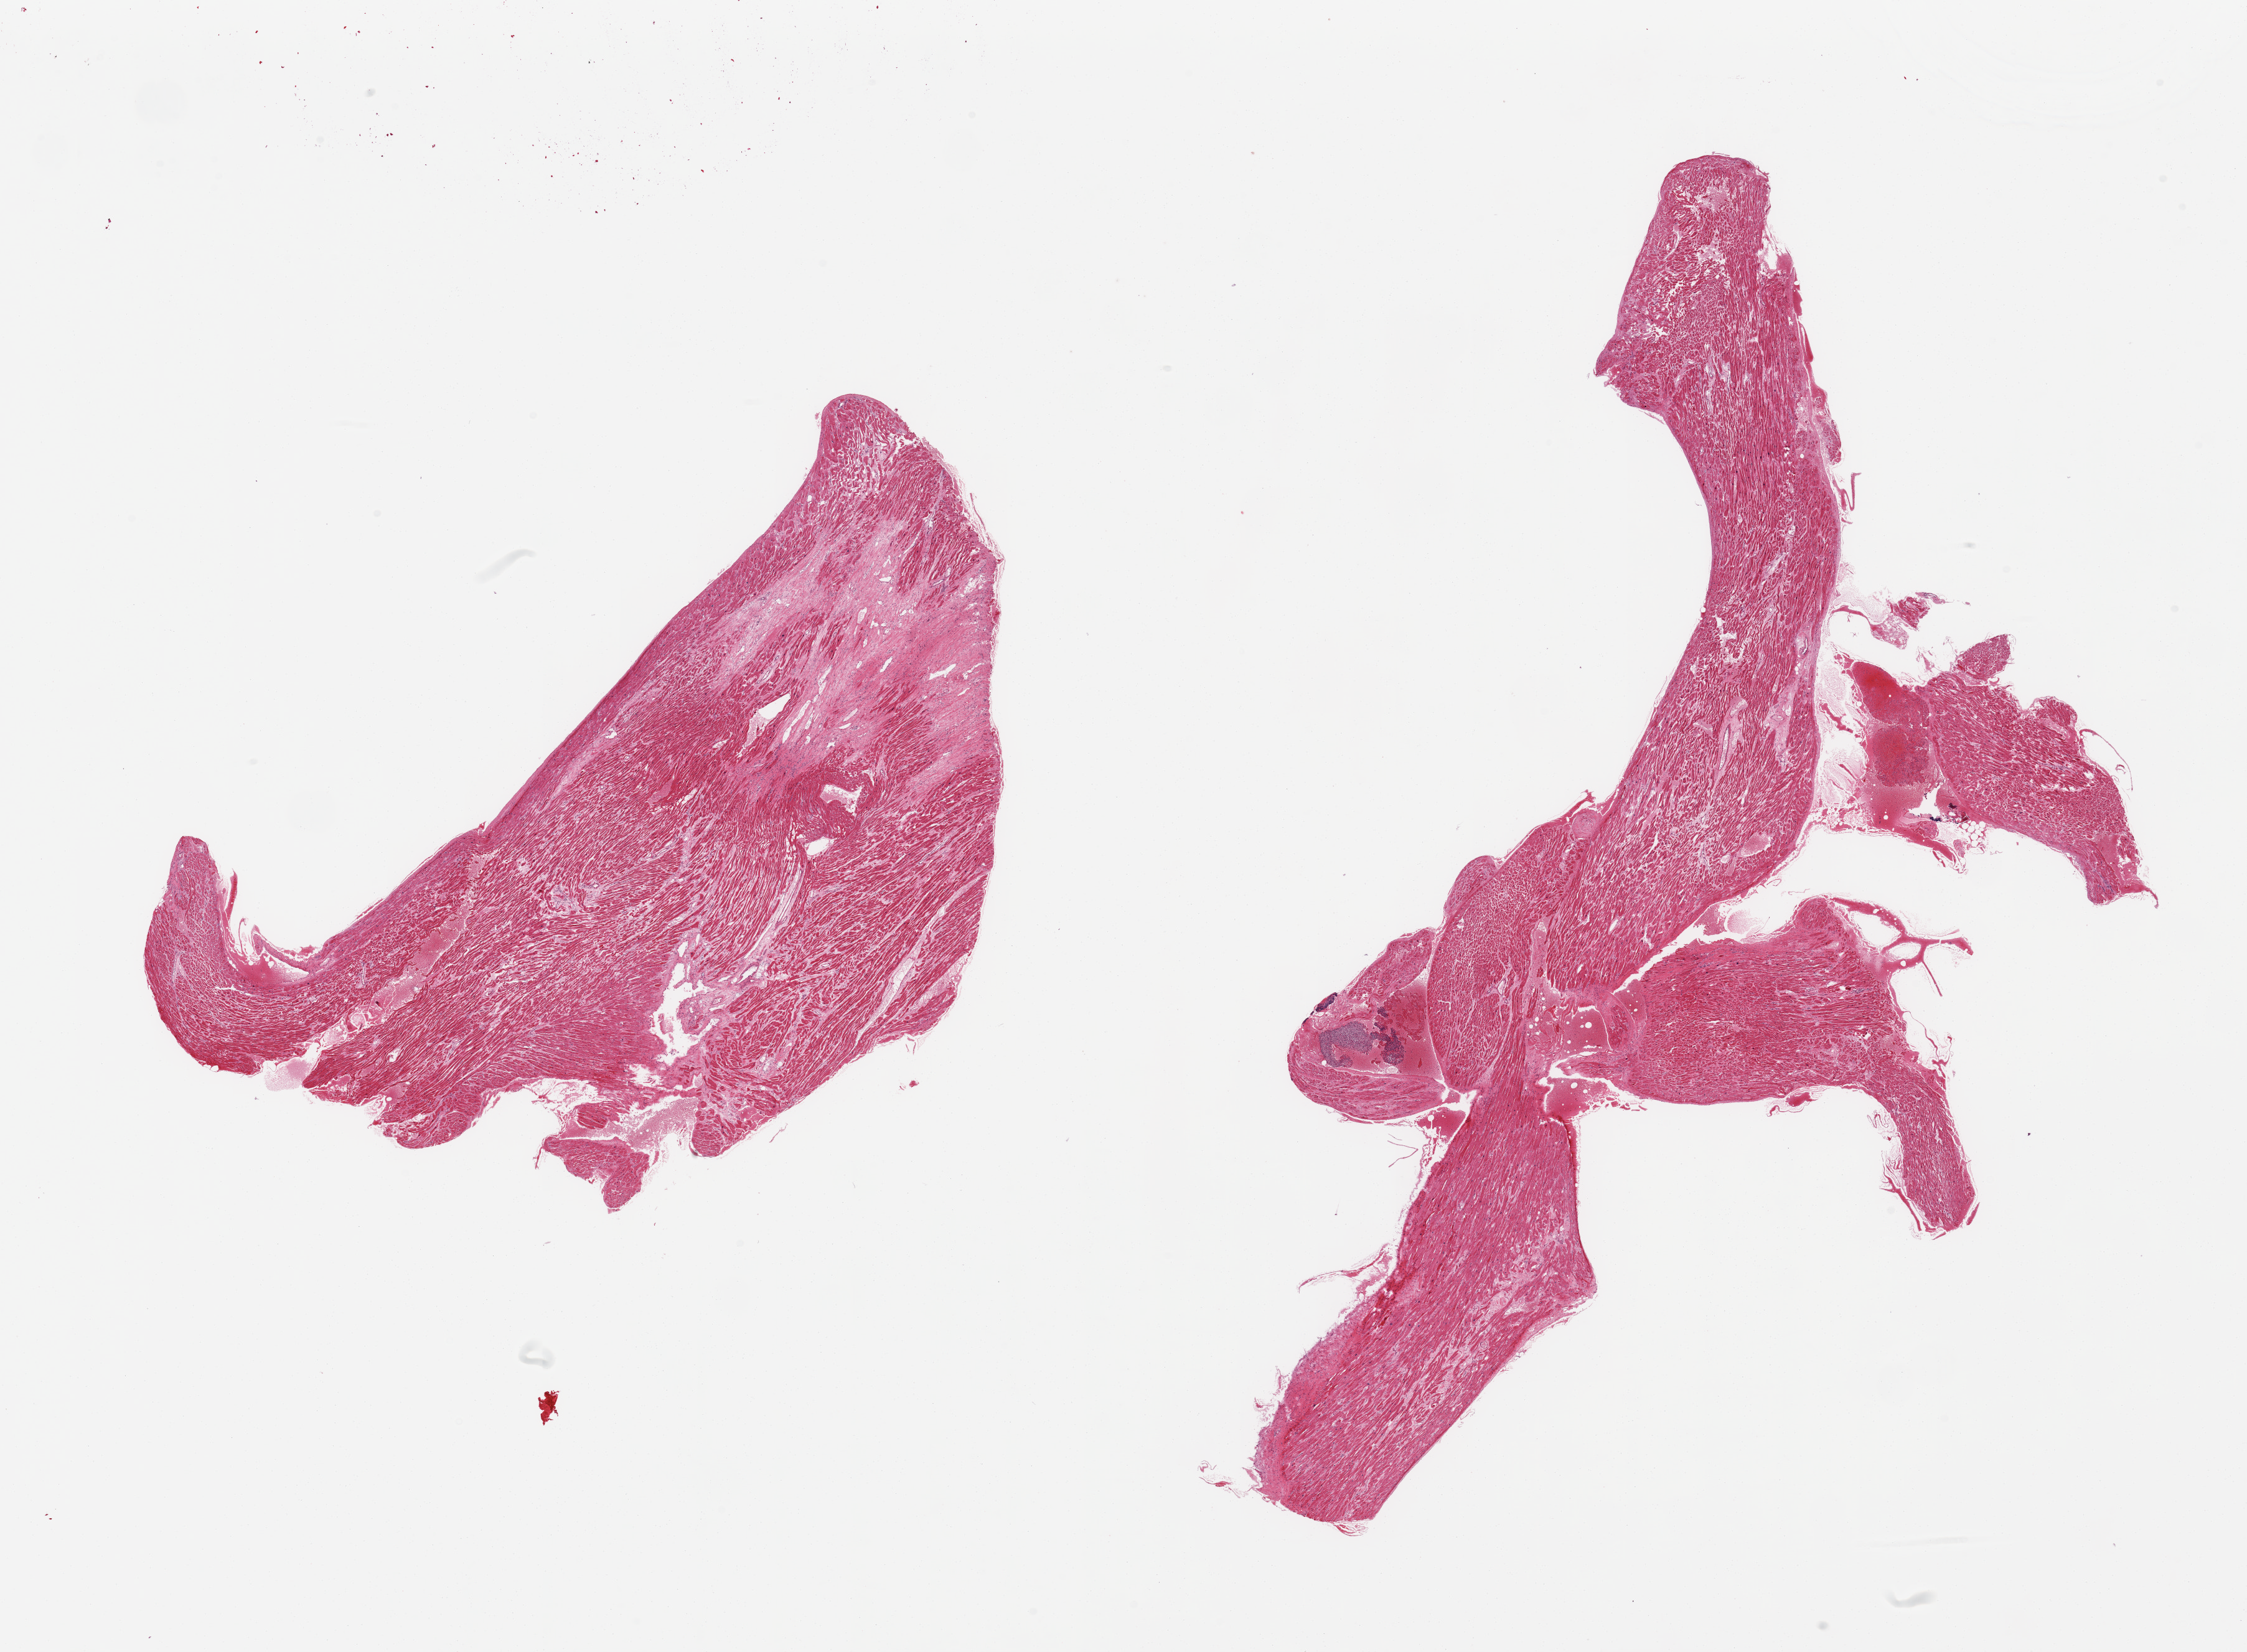
H&E whole-slide image, a low-resolution overview of the entire scanned area, about 28.5 x 21.0 mm (from a 20x scan), PAXgene-fixed paraffin-embedded (PFPE) section, target tissue: auricular appendage, tissue donor sample. Male donor.
Review note (as recorded): 2 pieces; 20% fibrous content in 1; clotted blood with numerous white blood cells in the other.